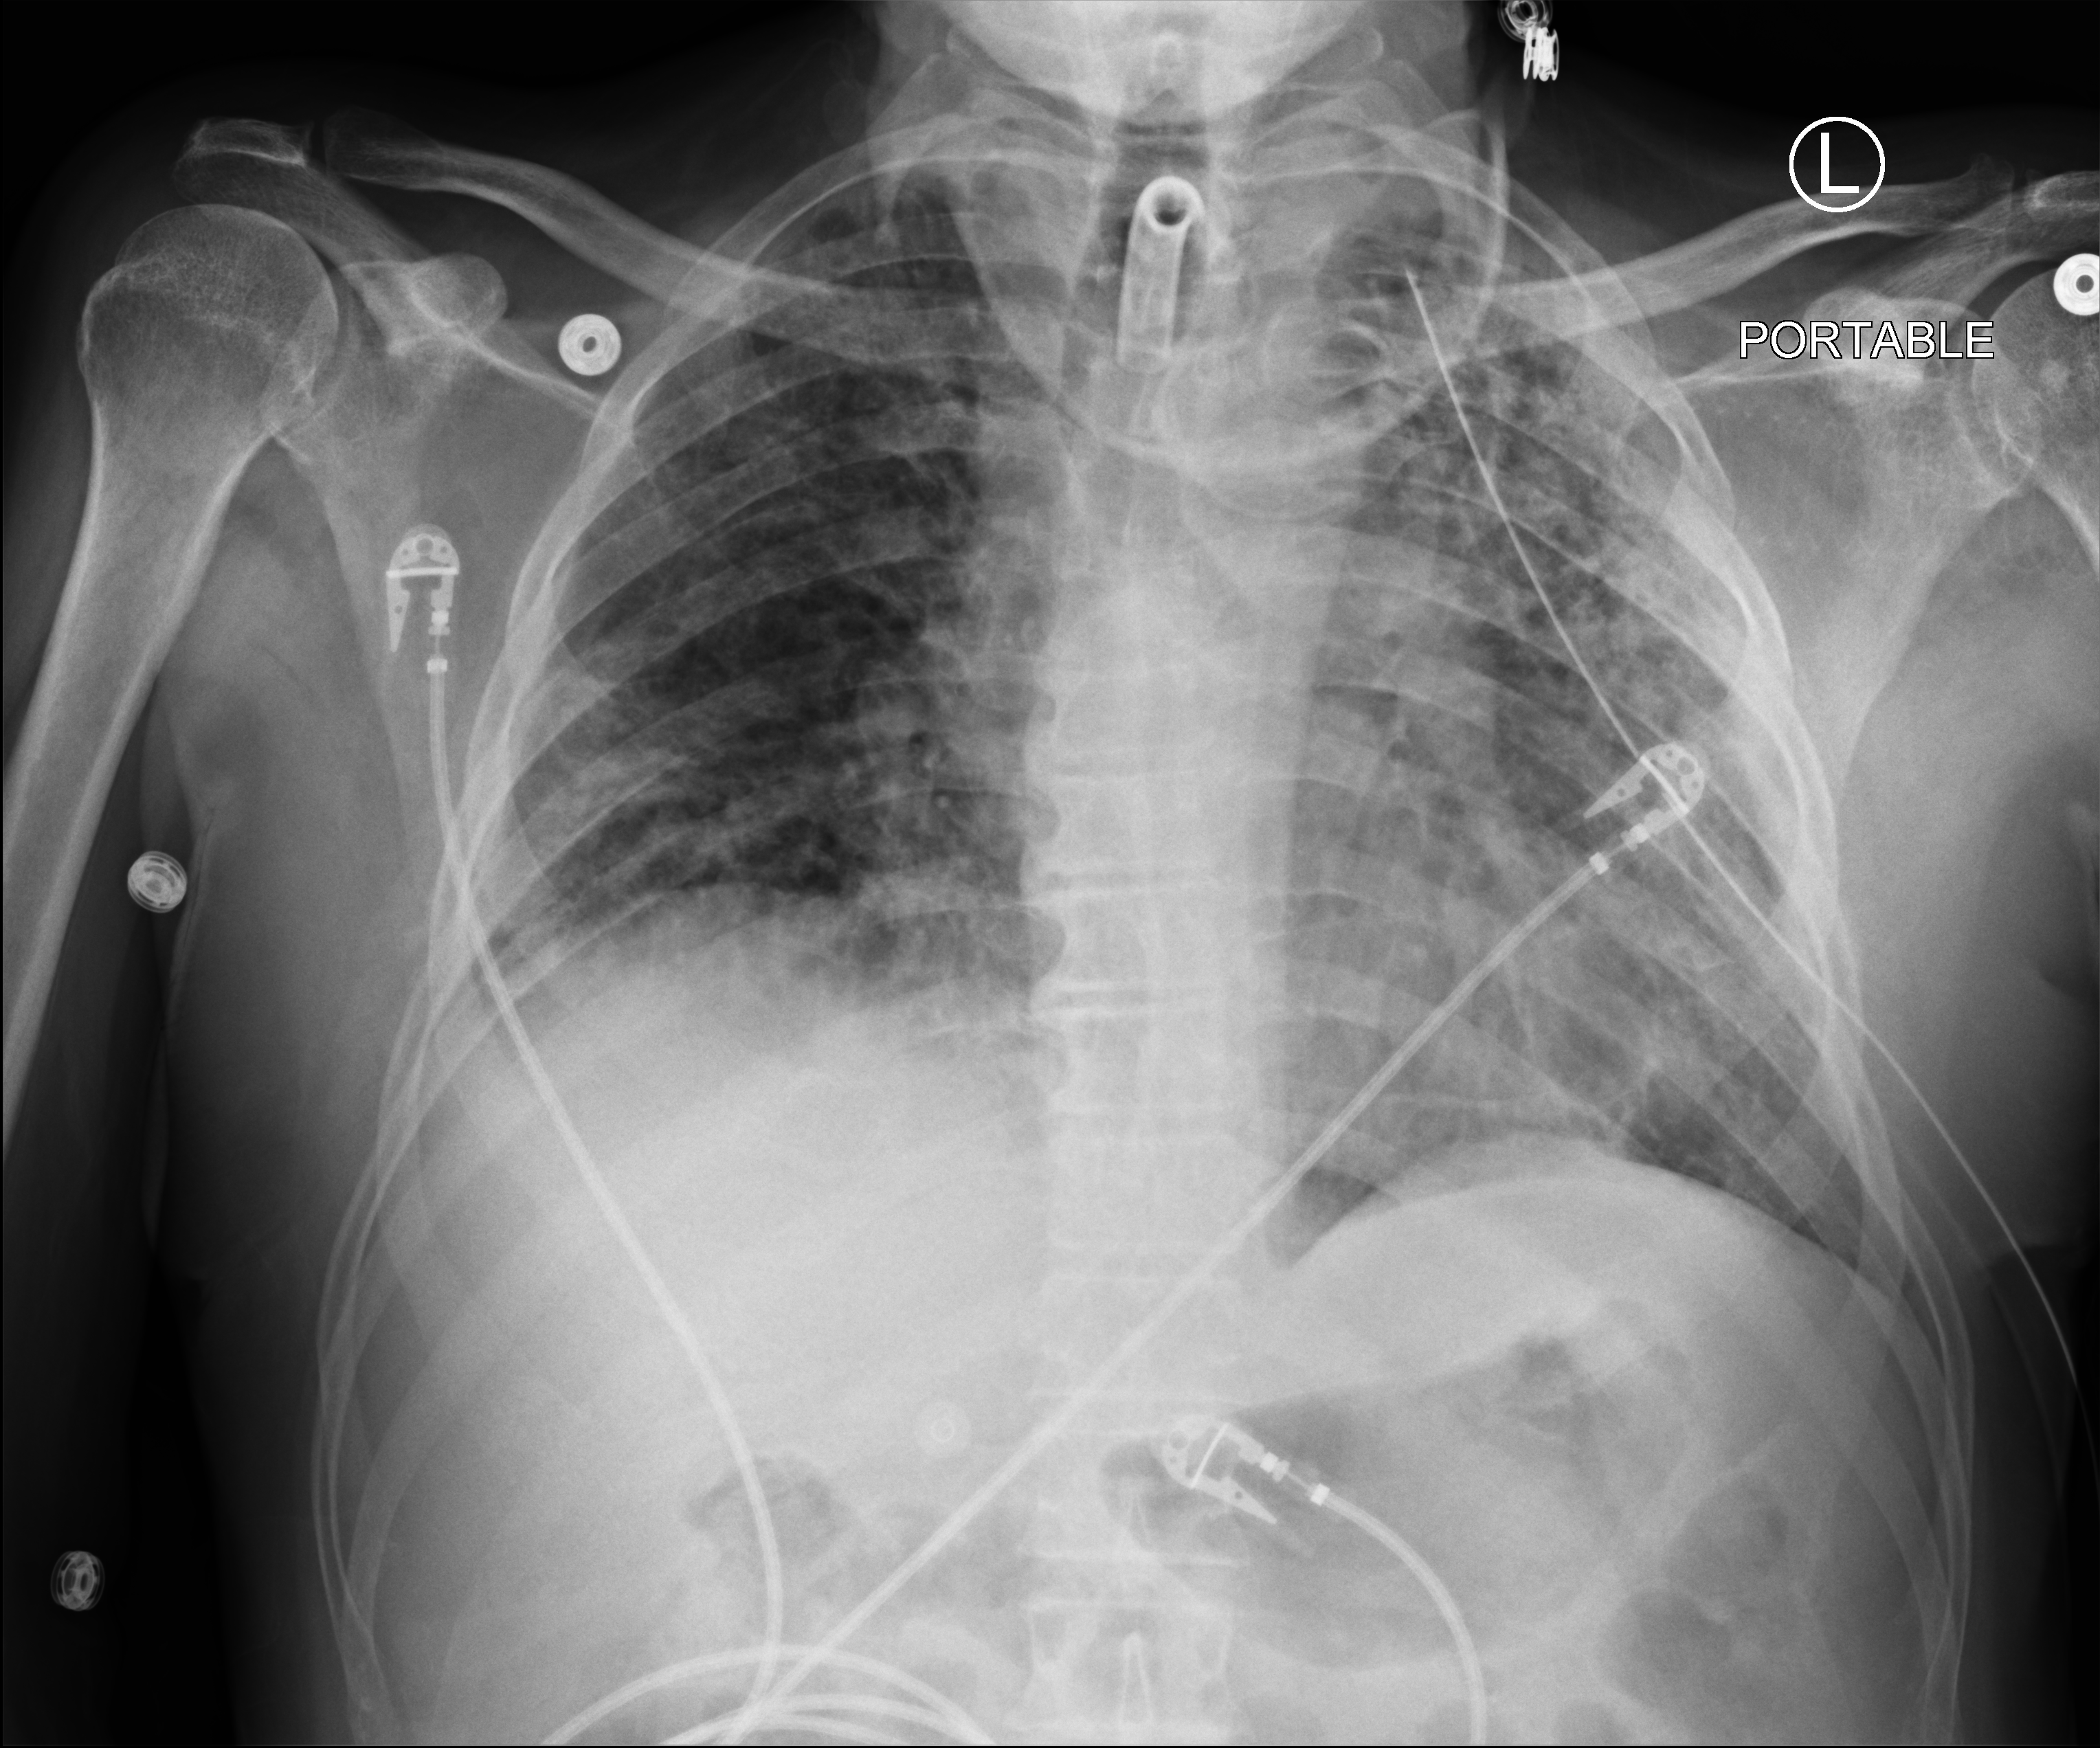
Chest X-ray (portable); anteroposterior (AP) projection. Male patient hospitalised with COVID-19, age 18–59 years.
Admission-level facts for this patient (not findings on this image; timing relative to this image not recorded): mechanically ventilated during this hospital stay: yes; length of hospital stay: 83 days; admitted to intensive care during this hospital stay: yes.